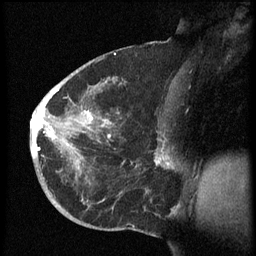
Breast MRI (dynamic contrast-enhanced), one sagittal slice; slice 33 of 60 in the series (ordered by position); dynamic contrast-enhanced series, image 2 of 3 at this slice position (ordered by acquisition); 1.5 T; TE 4.2 ms, TR 8.4 ms; 2.5 mm slice thickness; 256 × 256 image matrix. Female patient, age 38 years. Case-level facts recorded for this patient, not image findings: setting: breast cancer imaged before/during neoadjuvant chemotherapy; receptor status: HER2-positive.
Outlined on this slice (semi-automatic segmentation, software-assisted and operator-edited):
- analysis volume of interest (the breast-tissue region the enhancement analysis was run in; not a lesion): bounding box (x1, y1, x2, y2) in pixels: (31, 74, 173, 202)
- tumour enhancement mask (voxels above the 70 % enhancement threshold inside the analysis volume of interest): (31, 89, 173, 169)